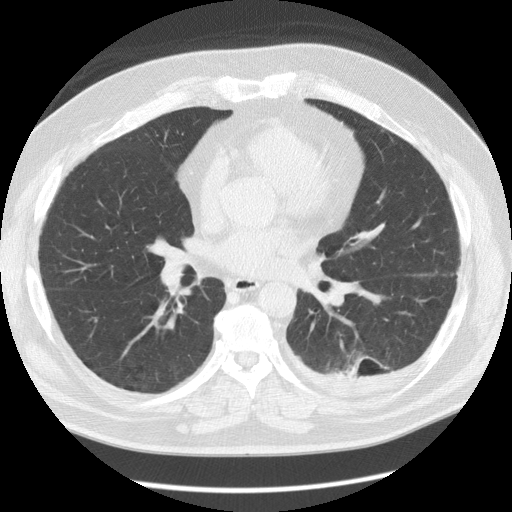
Chest CT (low-dose screening protocol), one axial image. Baseline screening round. Lung window (W 1500 / L -600 HU). Slice 62 of 126 in the series. Male participant, aged 56 years at enrolment.
Expert-annotated lung lesion, bounding box <325,343,398,395> (left, top, right, bottom; pixels). The screening reader recorded 4 non-calcified nodules or masses ≥4 mm on this exam (left lower lobe, left lower lobe, right middle lobe, left upper lobe); which of them this box marks is not recorded. Official screen result: positive, change unspecified: nodule(s) >= 4 mm or enlarging nodule(s), mass(es), or other non-specific abnormalities suspicious for lung cancer.